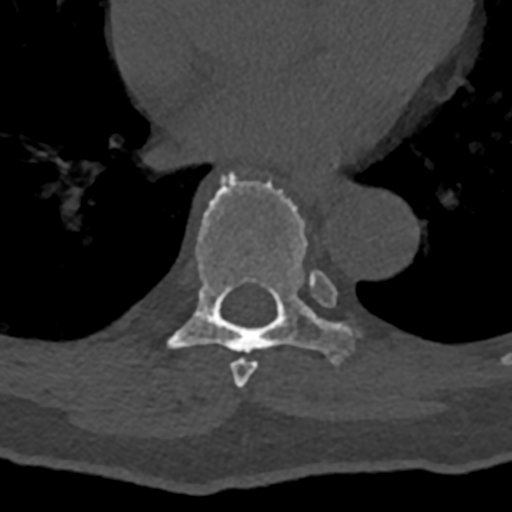
CT including the spine, one axial slice; slice 717 of 797 in the series (ordered by position); reconstruction kernel Br40s/3; bone window (W 1800 / L 400 HU); 512 × 512 image matrix, field of view 160 × 160 mm. Male patient, age 74 years. From the clinical record (not read from this slice): primary cancer: renal; vertebrae with lytic lesions (as recorded): T10, L1, L2, L3, L4, L5.
Annotated regions visible in this slice (semi-automatic segmentation, software-assisted and operator-edited):
- T7 vertebra: bounding box <230,271,334,388> (left, top, right, bottom; pixels)
- T8 vertebra: <163,169,353,363>